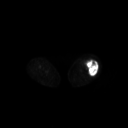
FDG PET of an extremity soft-tissue mass (from a PET/CT study), one axial slice; slice 210 of 267 in the series (ordered by position); 128 × 128 image matrix, field of view 700 × 700 mm. Female patient, age 62 years. From the clinical record (not read from this slice): histological type: undifferentiated – high grade; grade: high; site of the primary tumour: left thigh.
Structures marked on this image (expert contour drawn on MRI and transferred to this co-registered scan by the dataset authors):
- gross tumour volume including surrounding oedema: bounding box <83,59,99,76> (left, top, right, bottom; pixels)
- gross tumour volume (mass): <85,59,98,76>